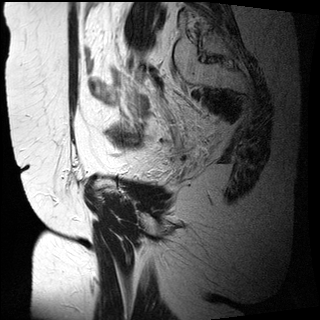
Pelvic MRI for cervical cancer, one sagittal slice. Position 22 of 27 along the scan axis. T2-weighted. 1.5 T. TE 89 ms, TR 2740 ms. 4 mm slice thickness. 320 × 320 image matrix. Female patient, age 47 years.
Outlined on this slice (outlined manually by an expert reader):
- uterus and cervix: bounding box [x1, y1, x2, y2] px = [104, 124, 147, 150]